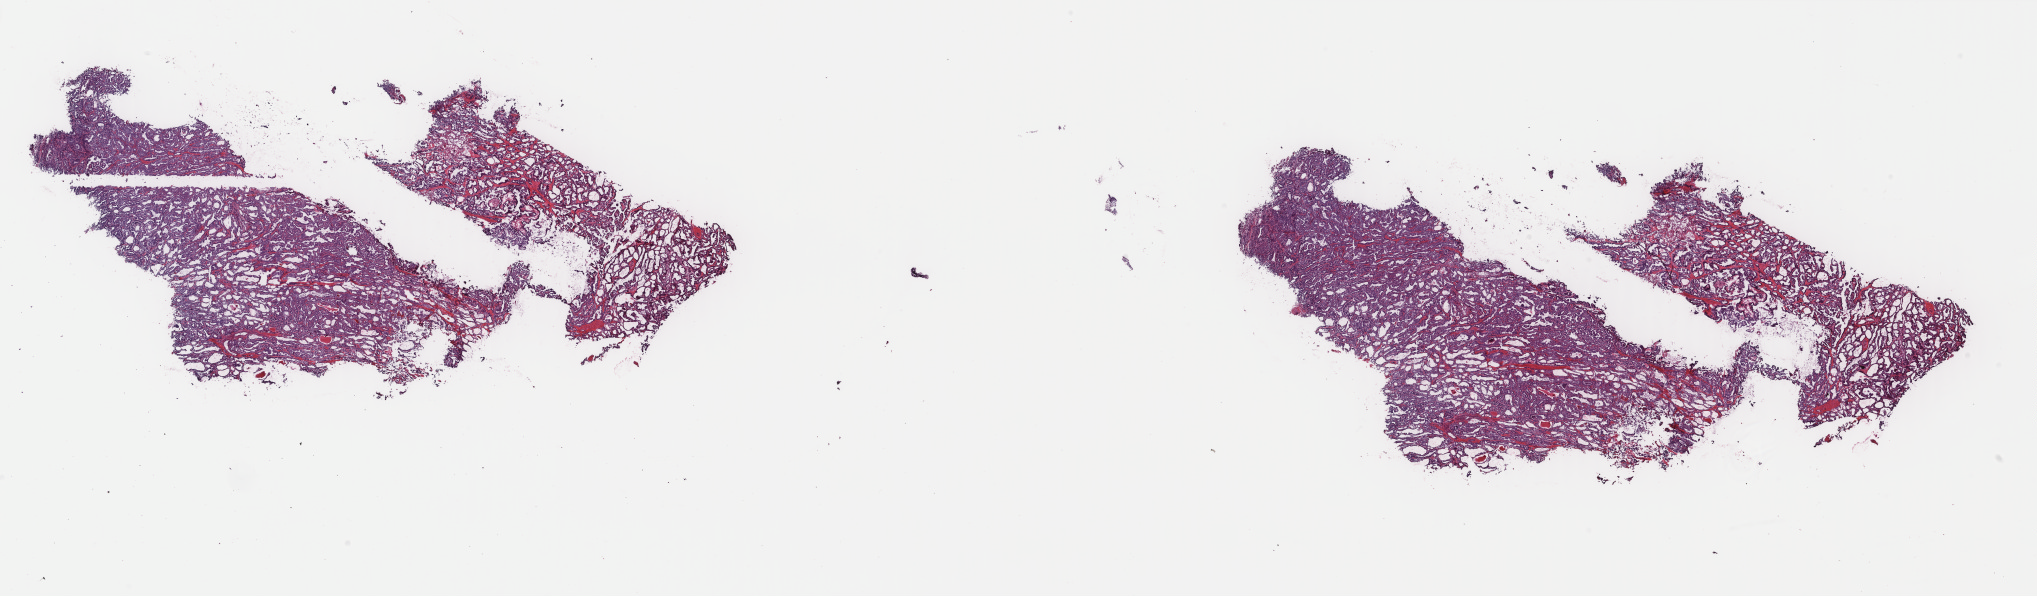
Whole-slide histology image, H&E, low-resolution overview of the scanned area, about 32.3 x 9.5 mm (acquisition: 40x scan). Frozen section from the top of the tissue portion. Primary tumour sample from the thyroid. Patient: female, age at initial diagnosis 48 years. Composition of this section per pathologist review: tumour cells 100%, tumour nuclei 95%, normal cells 0%, stromal cells 0%, necrosis 0%. Inflammatory infiltration, as recorded: lymphocyte infiltration 0%, monocyte infiltration 0%, neutrophil infiltration 0%.
AJCC pathologic stage: III (6th edition). Laterality: left. Histologic diagnosis: Papillary adenocarcinoma, NOS (thyroid gland).